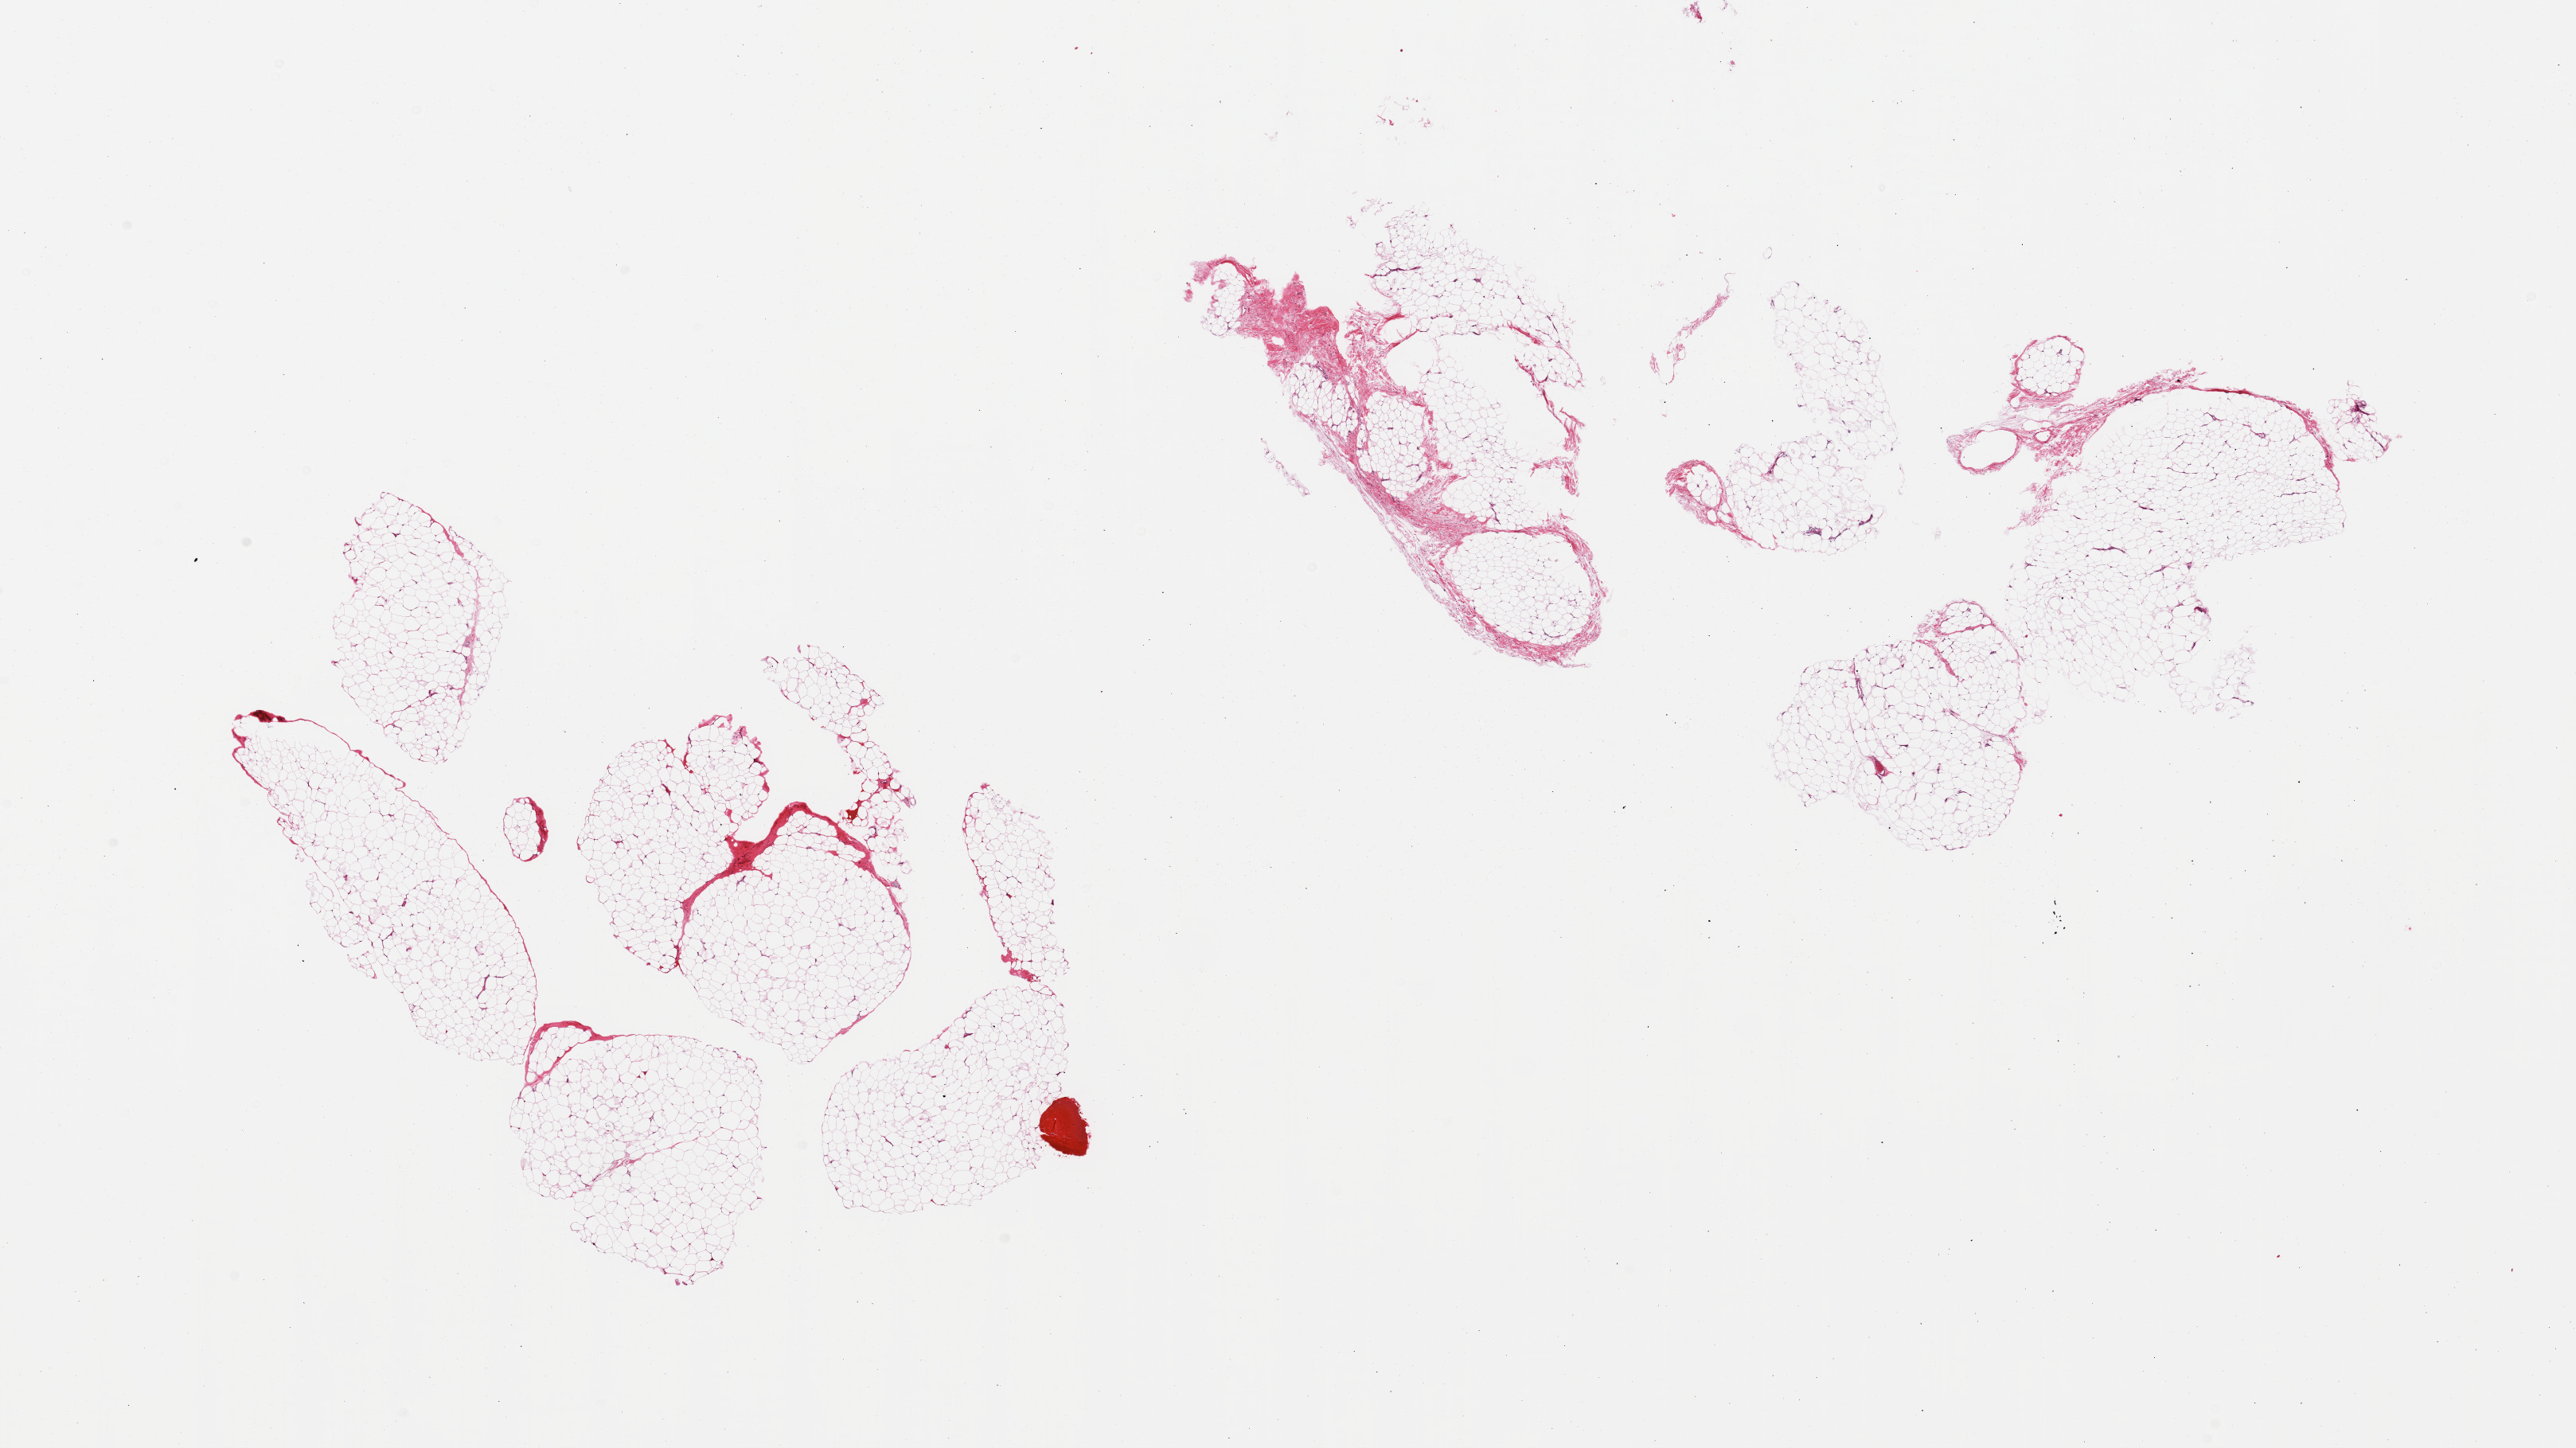
Digitized H&E-stained section, low-resolution overview of the scanned area, about 25.6 x 14.4 mm, PAXgene-fixed paraffin-embedded (PFPE) section, section of adipose tissue (target tissue), tissue donor sample. Male donor.
Reviewer comment on this tissue sample: 2 pieces (fragmented); mature adipose tissue and fibrovascular component.